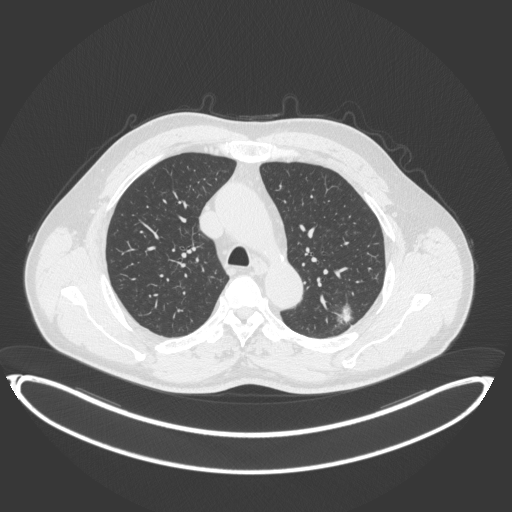
Chest CT, one axial slice; slice 256 of 399 in the series (ordered by position); 120 kVp; lung window (W 1500 / L -600 HU); 1 mm slice thickness; 512 × 512 image matrix, field of view 469 × 469 mm. Male patient, age 58 years. Case-level facts recorded for this patient, not image findings: clinical TNM (as recorded): T1c N0 M0; histopathological grade: G1-2.
Outlined on this slice (rectangle marked by the reading radiologist):
- lung tumour (recorded histology: adenocarcinoma): bounding box (x1, y1, x2, y2) in pixels: (334, 300, 358, 328)